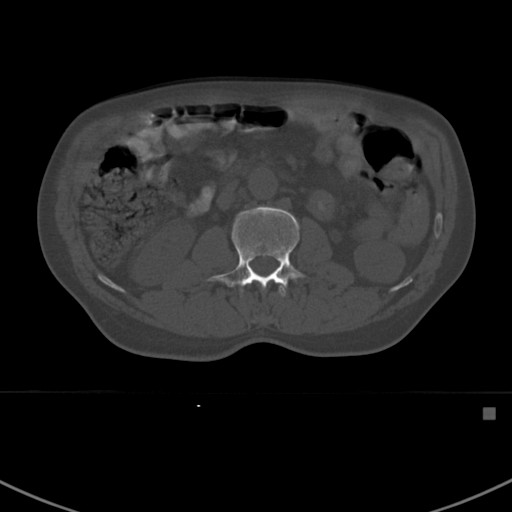
CT including the spine, one axial slice; slice 287 of 412 in the series (ordered by position); reconstruction kernel Br40s; 120 kVp; bone window (W 1800 / L 400 HU); 1.5 mm slice thickness; 512 × 512 image matrix. Male patient, age 59 years. Case-level facts recorded for this patient, not image findings: primary cancer: prostate.
Annotated regions visible in this slice (semi-automatically segmented with operator editing):
- L1 vertebra: bounding box [x1, y1, x2, y2] px = [279, 287, 283, 296]
- L2 vertebra: [208, 206, 305, 296]